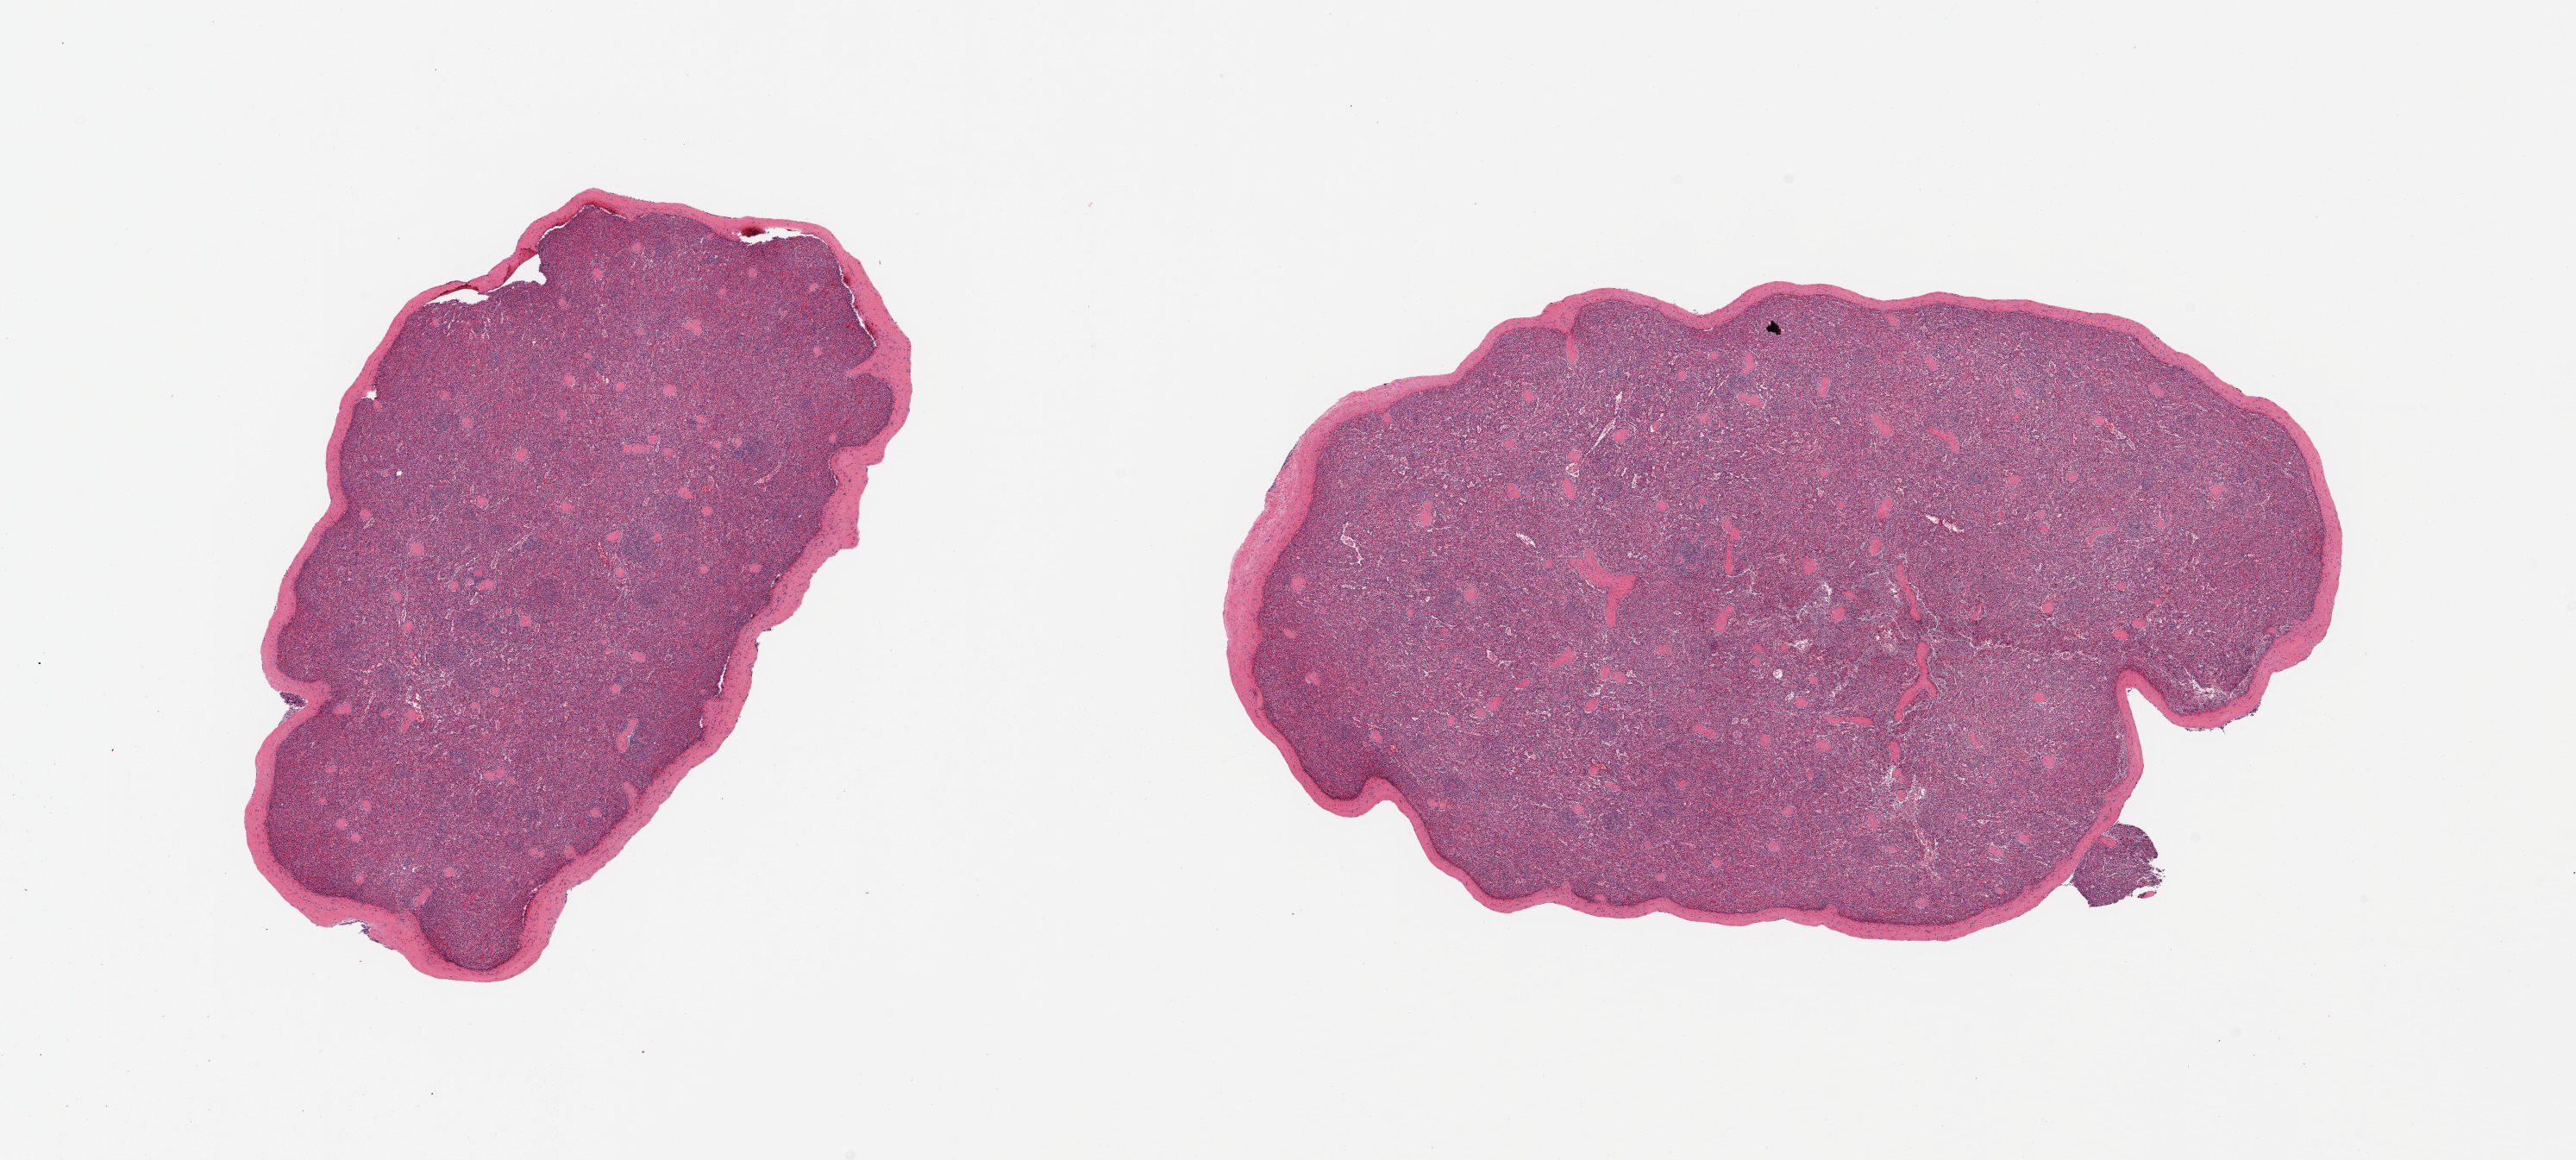
Hematoxylin and eosin (H&E) whole-slide image — whole scanned area (about 23.6 x 10.6 mm, acquisition: 20x scan) shown as a low-resolution overview; PAXgene-fixed paraffin-embedded (PFPE) section; target tissue: spleen; tissue donor sample. Donor sex: female.
Reviewer comment on this tissue sample: 2 pieces; includes capsule (target is 5mm below capsule).